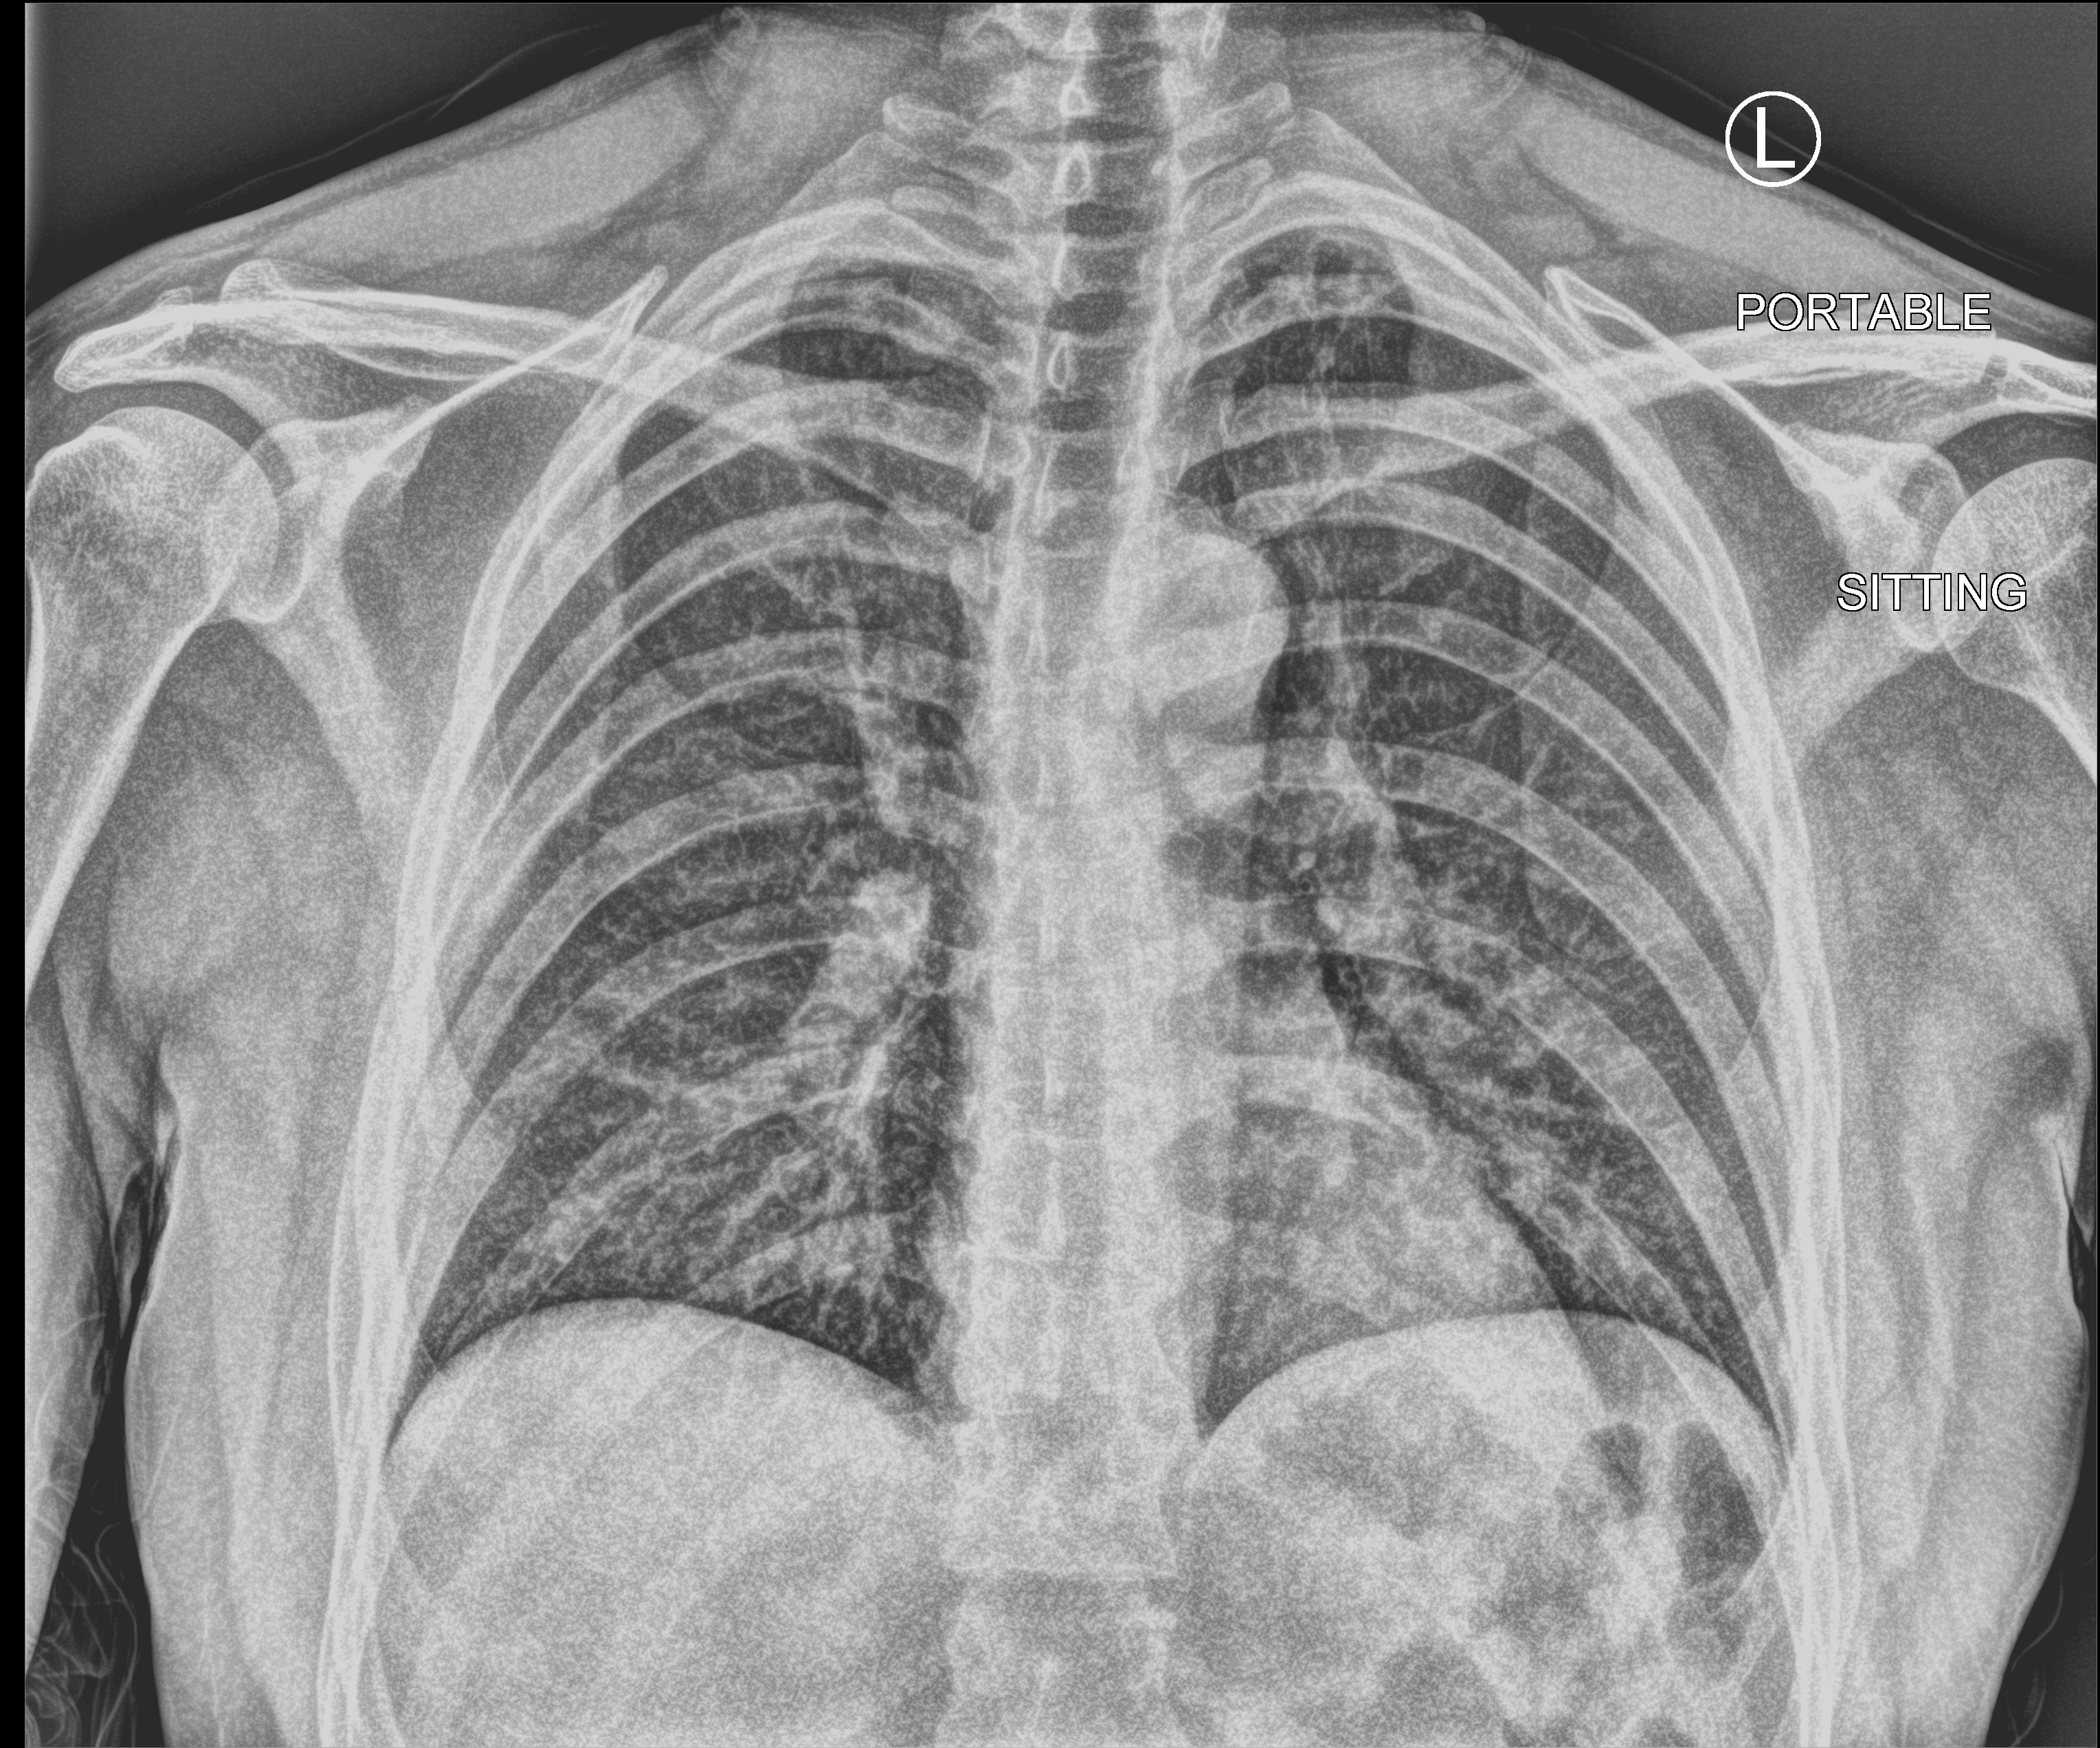
Bedside chest radiograph (computed radiography), anteroposterior (AP) projection. Patient hospitalised with COVID-19; male, aged 18–59 years.
From the hospital-stay record, not from the radiograph (when in the stay this image was taken is not recorded): length of hospital stay: 7 days; mechanically ventilated during this hospital stay: no; admitted to intensive care during this hospital stay: no.